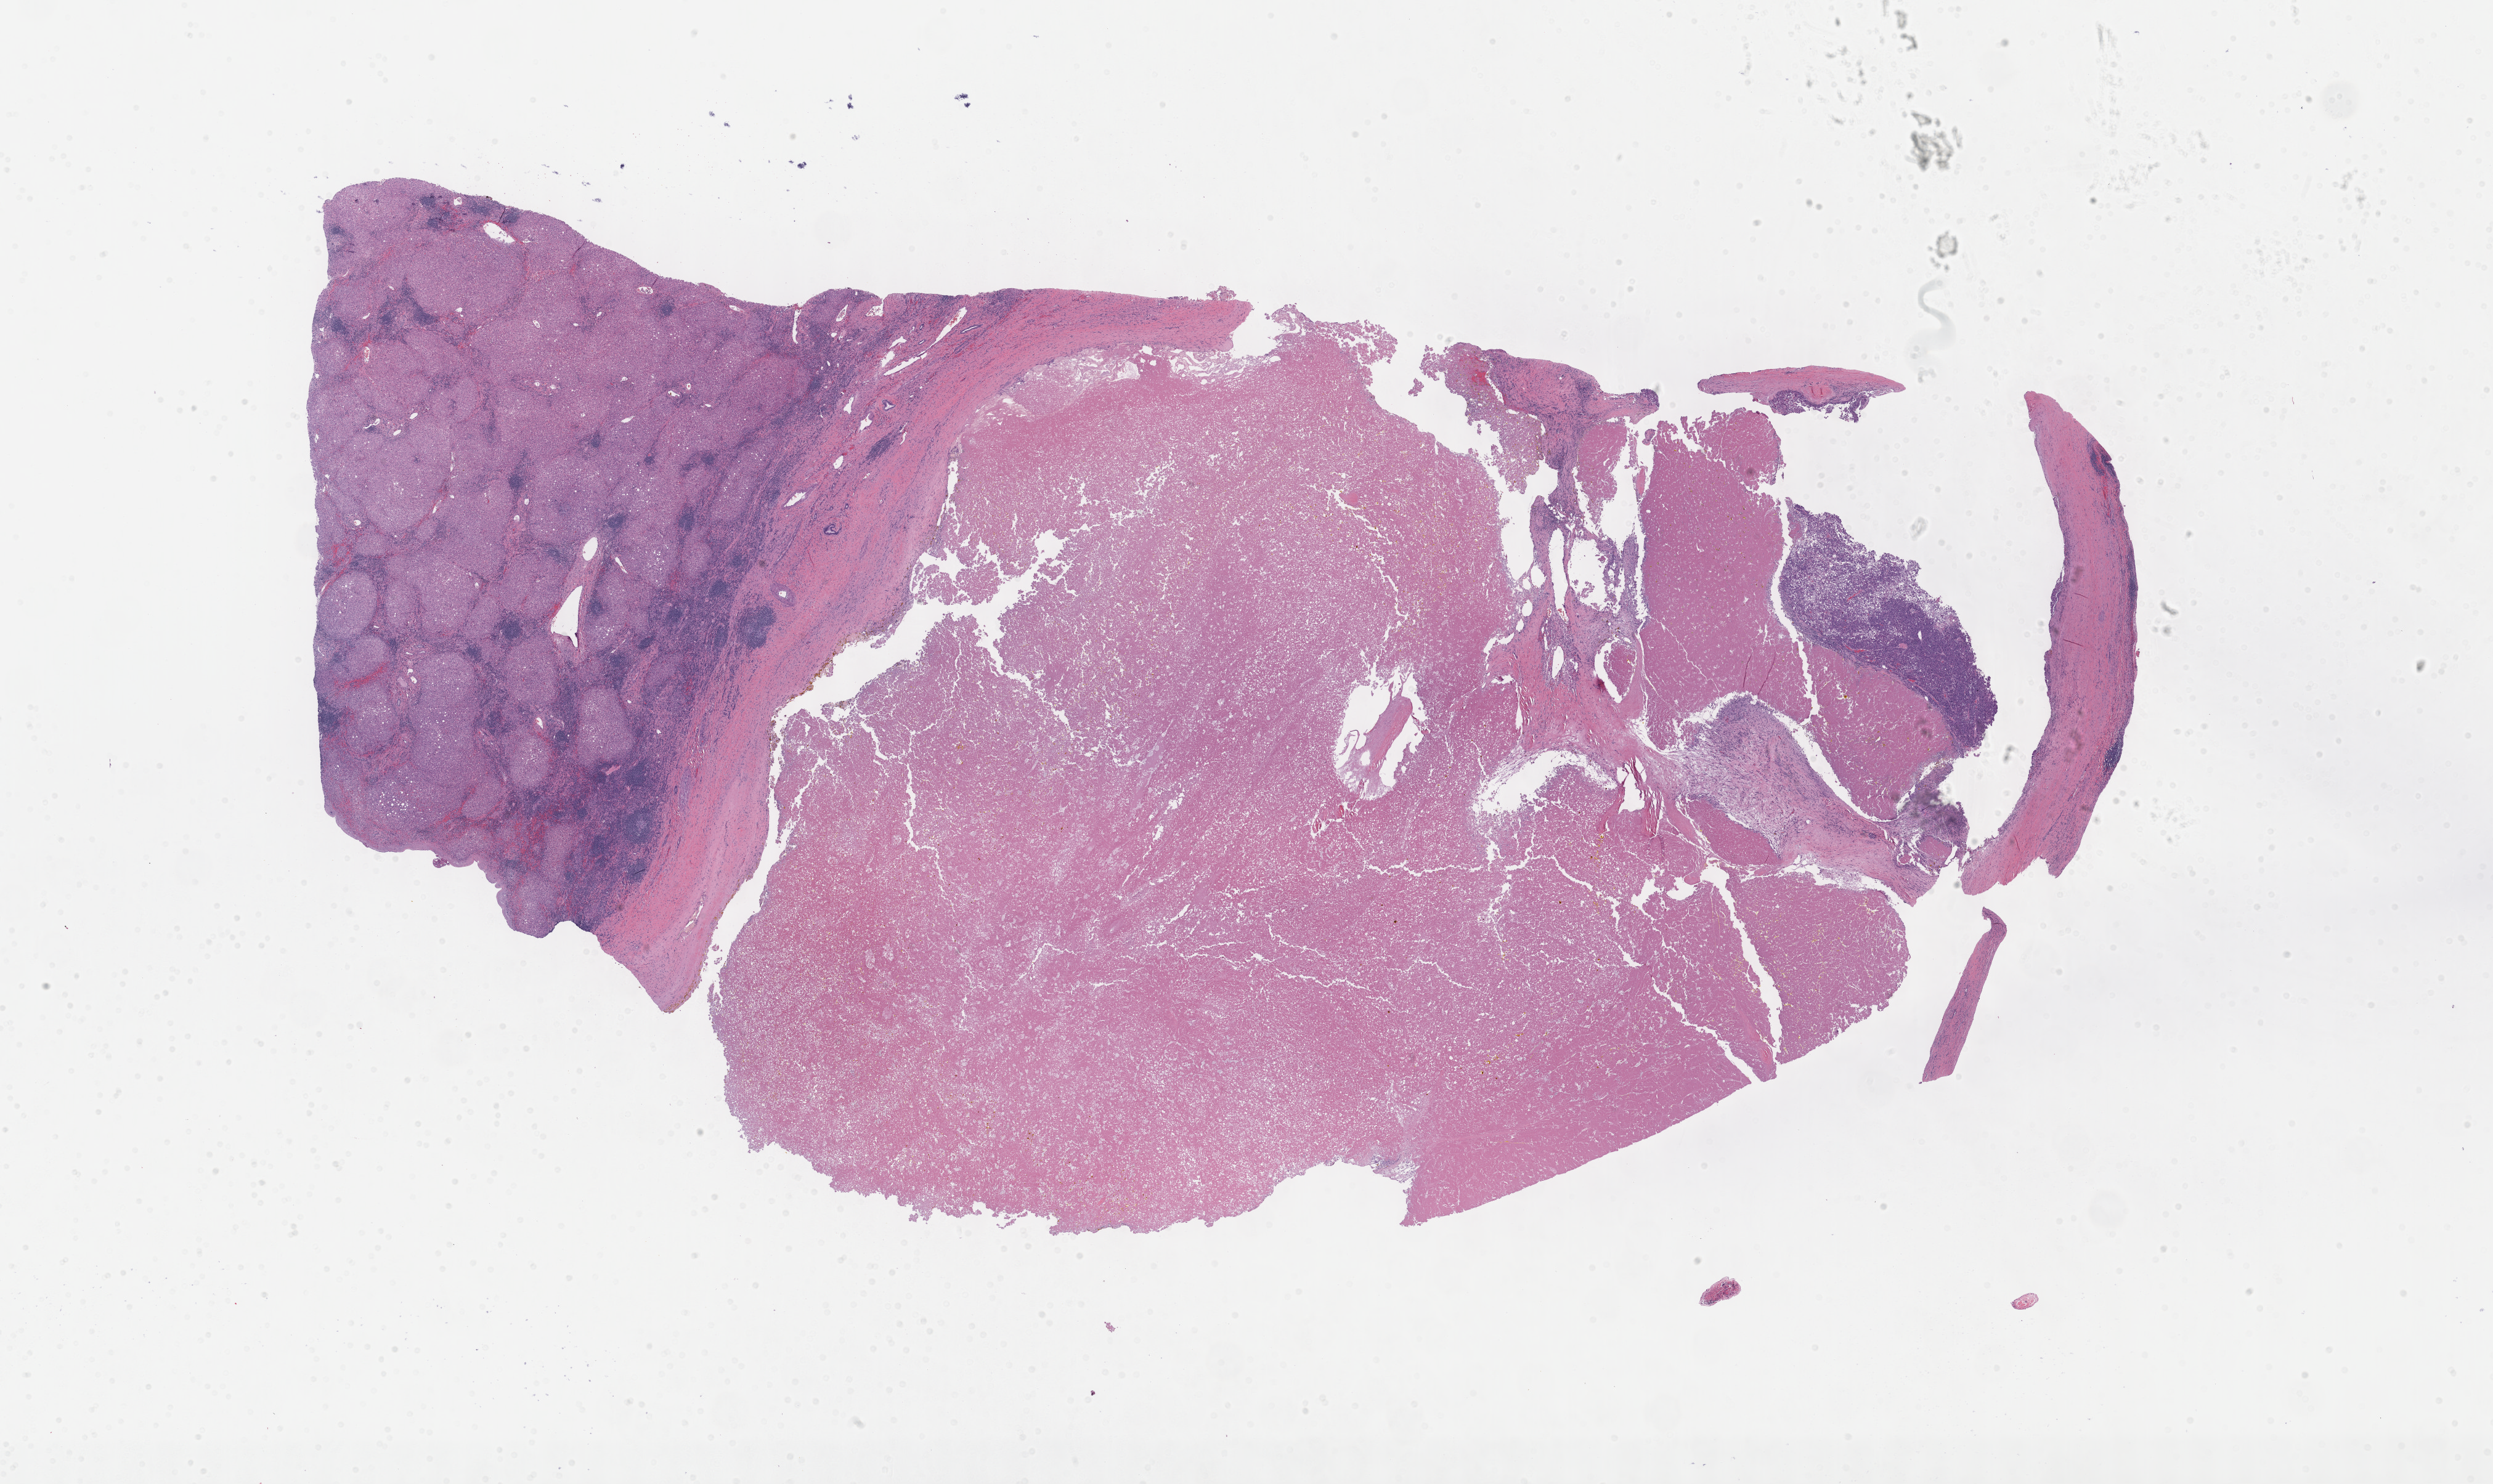
Digitized H&E tissue section (whole slide), shown as a low-resolution overview of the whole scanned area (about 32.7 x 19.5 mm, from a 40x scan); formalin-fixed paraffin-embedded (FFPE) diagnostic section; liver, primary tumour sample. Male, age 64 years at initial diagnosis. Histologic grade: G3 (poorly differentiated).
TNM: T1 N0 M0. AJCC pathologic stage: I (7th edition). Histologic diagnosis: Hepatocellular carcinoma, NOS.